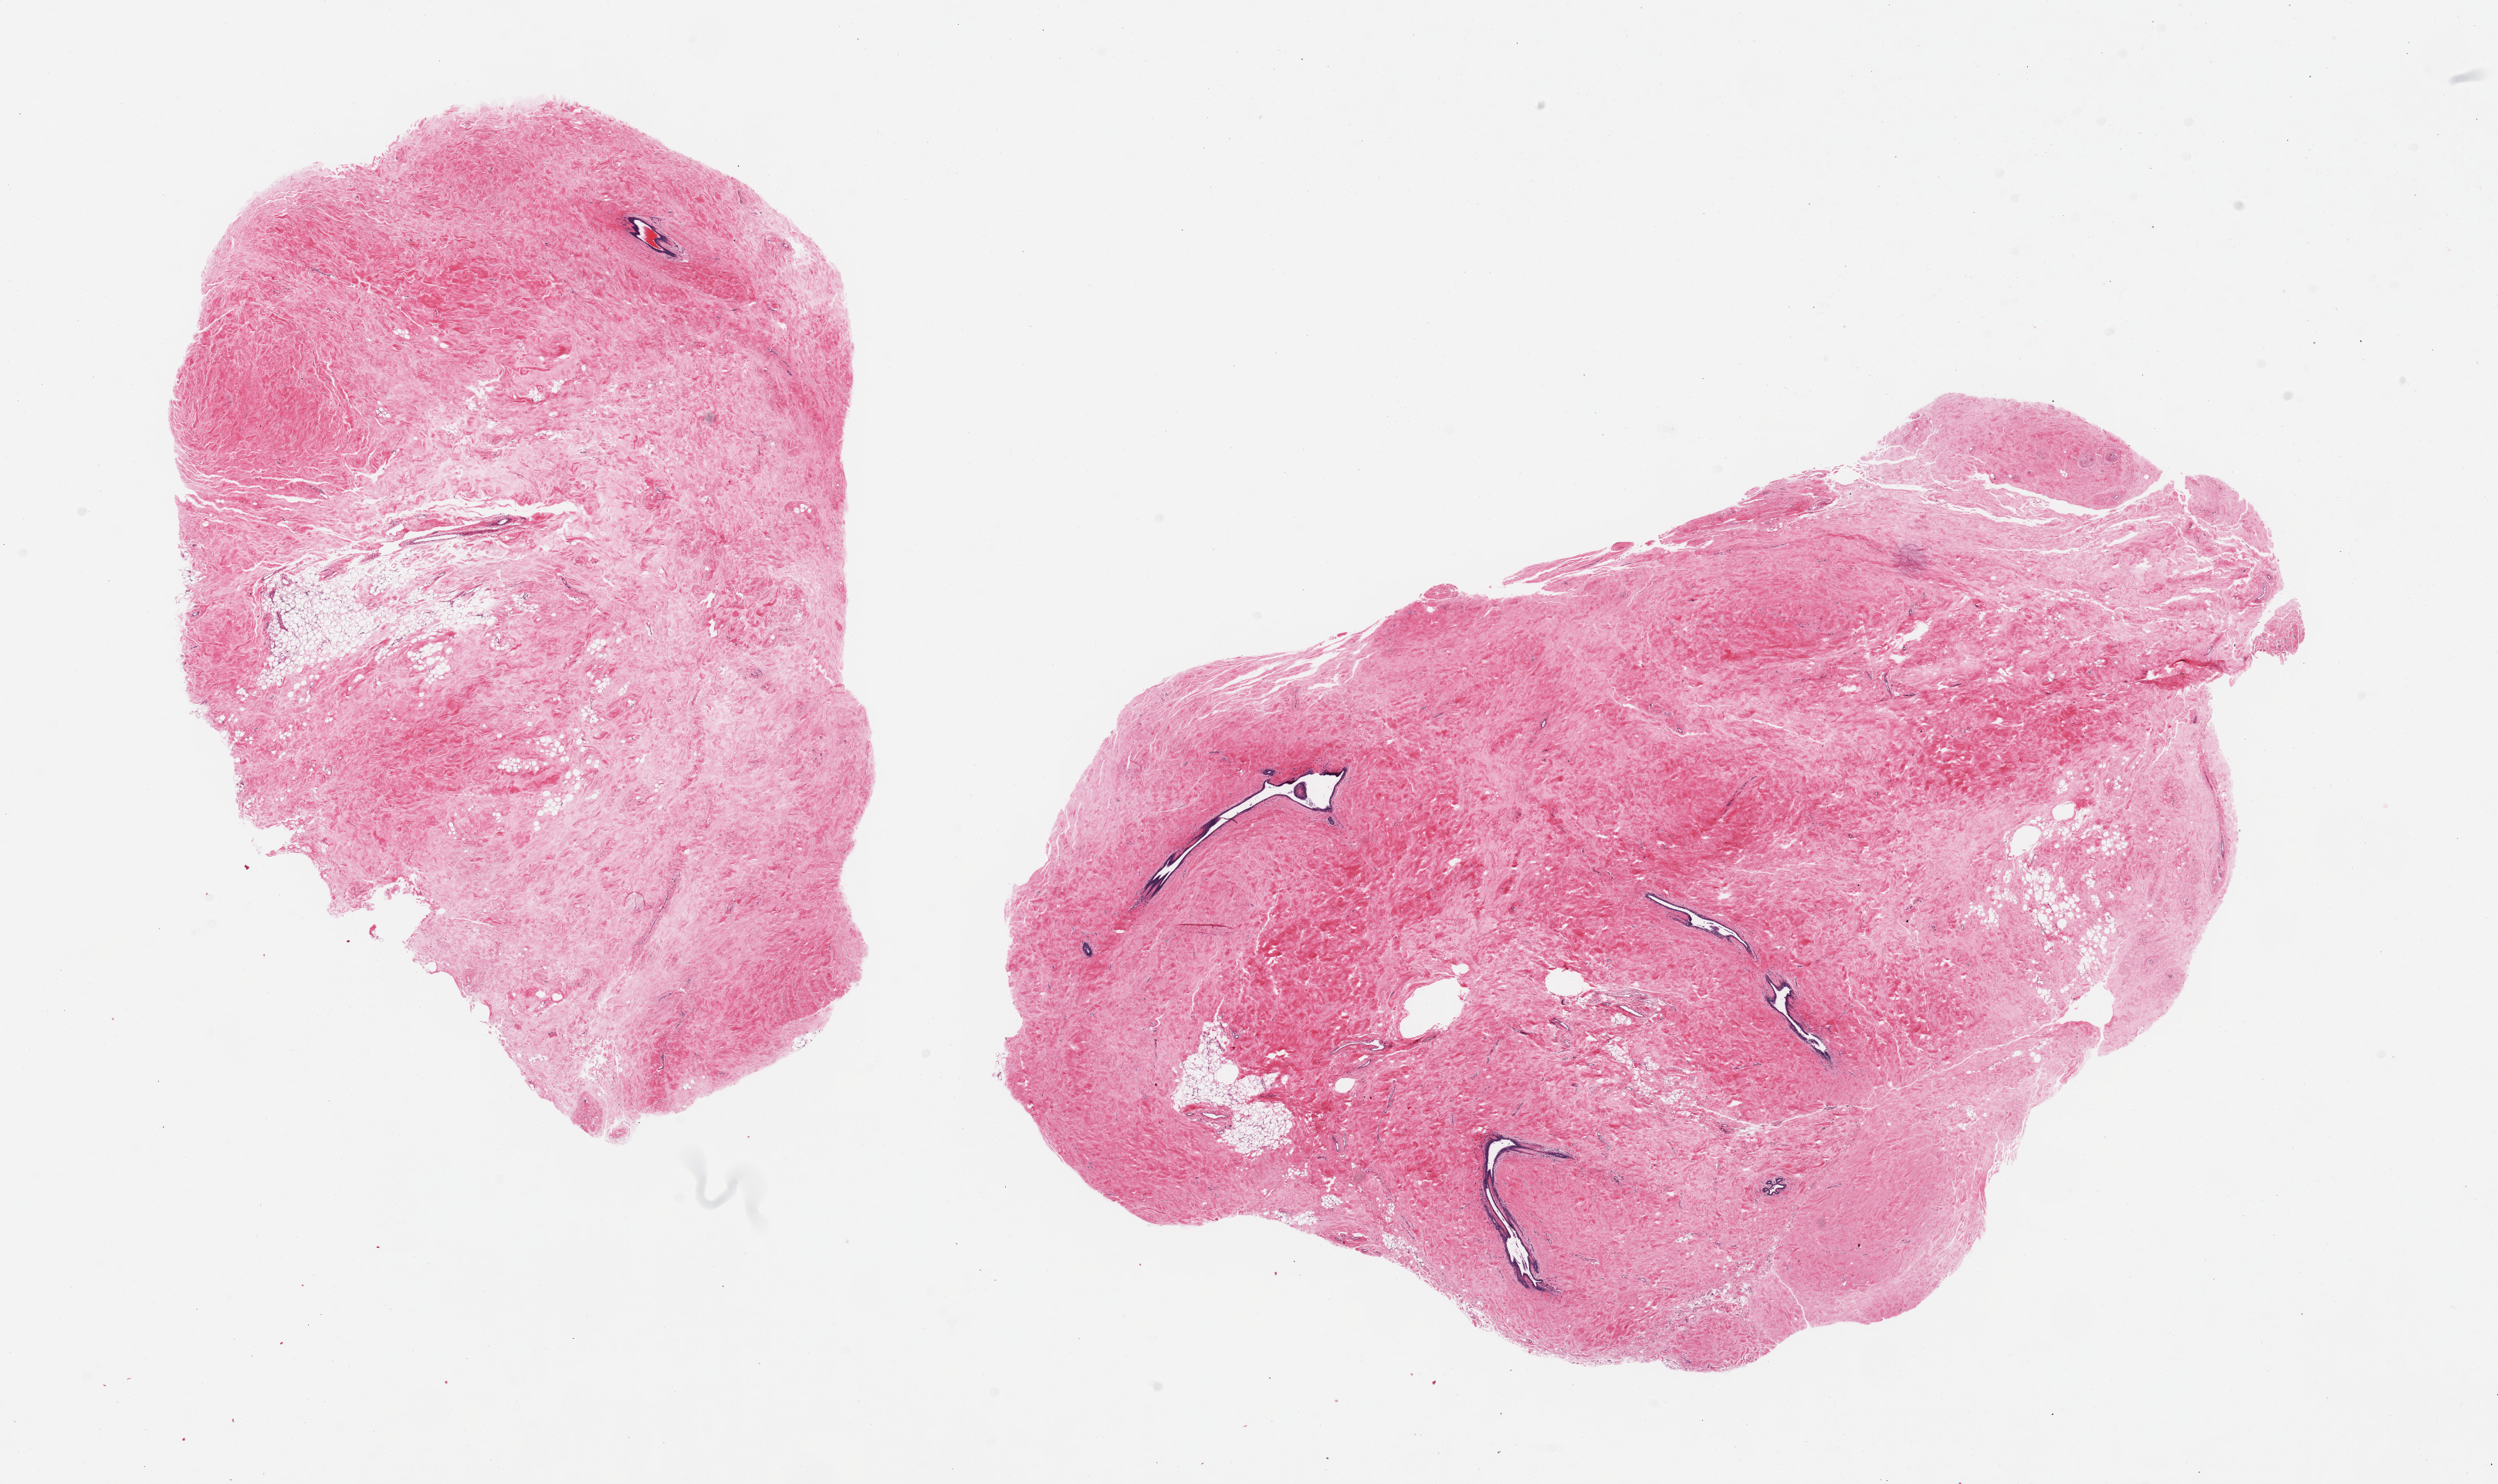
Digitized haematoxylin and eosin-stained section, a low-resolution overview of the entire scanned area, about 25.6 x 15.2 mm; PAXgene-fixed paraffin-embedded (PFPE) section; target tissue: breast; donor tissue sample. Donor: female.
• reviewer comment on this tissue sample: 2 pieces, fibrous mastopathy